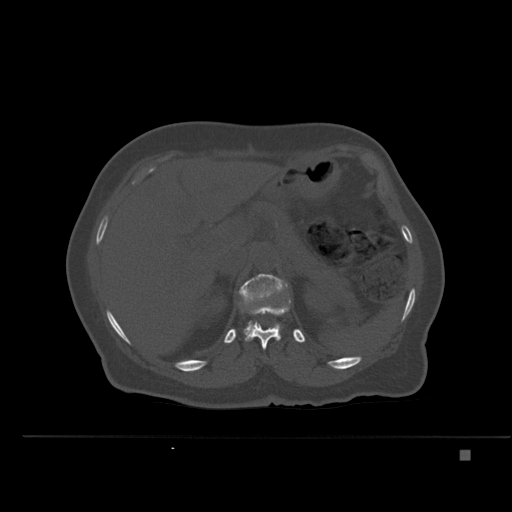
CT including the spine, one axial slice. Position 249 of 477 along the scan axis. Bone window (W 1800 / L 400 HU). 1.5 mm slice thickness. 512 × 512 image matrix, field of view 422 × 422 mm. Female patient, age 74 years. From the clinical record (not read from this slice): primary cancer: colon.
Annotated regions visible in this slice (semi-automatic segmentation, software-assisted and operator-edited):
- L1 vertebra: bounding box <239,274,288,341> (left, top, right, bottom; pixels)
- T12 vertebra: <242,300,291,350>